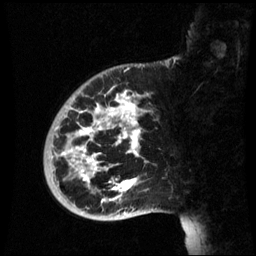
Breast MRI (dynamic contrast-enhanced), one sagittal slice; position 15 of 60 along the scan axis; dynamic contrast-enhanced series, image 2 of 3 at this slice position (ordered by acquisition); 1.5 T; TE 4.2 ms, TR 8.9 ms; 256 × 256 image matrix, field of view 220 × 220 mm. Female patient, age 35 years. Case-level facts recorded for this patient, not image findings: setting: breast cancer imaged before/during neoadjuvant chemotherapy; receptor status: HR-positive, HER2-negative.
Annotated regions visible in this slice (semi-automatic segmentation, software-assisted and operator-edited):
- analysis volume of interest (the breast-tissue region the enhancement analysis was run in; not a lesion): bounding box (x1, y1, x2, y2) in pixels: (43, 74, 164, 221)
- tumour enhancement mask (voxels above the 70 % enhancement threshold inside the analysis volume of interest): (60, 92, 141, 205)